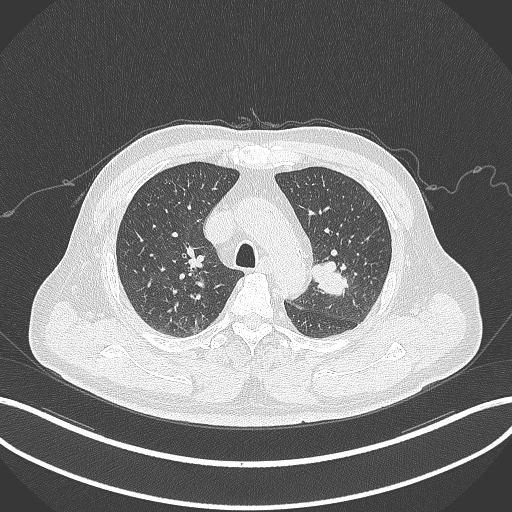
Chest CT, one axial slice; slice 222 of 286 in the series (ordered by position); reconstruction kernel B70f; lung window (W 1500 / L -600 HU); 512 × 512 image matrix, field of view 400 × 400 mm. Patient: male, 67 years. Case-level facts recorded for this patient, not image findings: clinical TNM (as recorded): T2a N1 M0.
Annotated regions visible in this slice (bounding box drawn by a radiologist):
- lung tumour (recorded histology: adenocarcinoma): bounding box <308,258,352,300> (left, top, right, bottom; pixels)